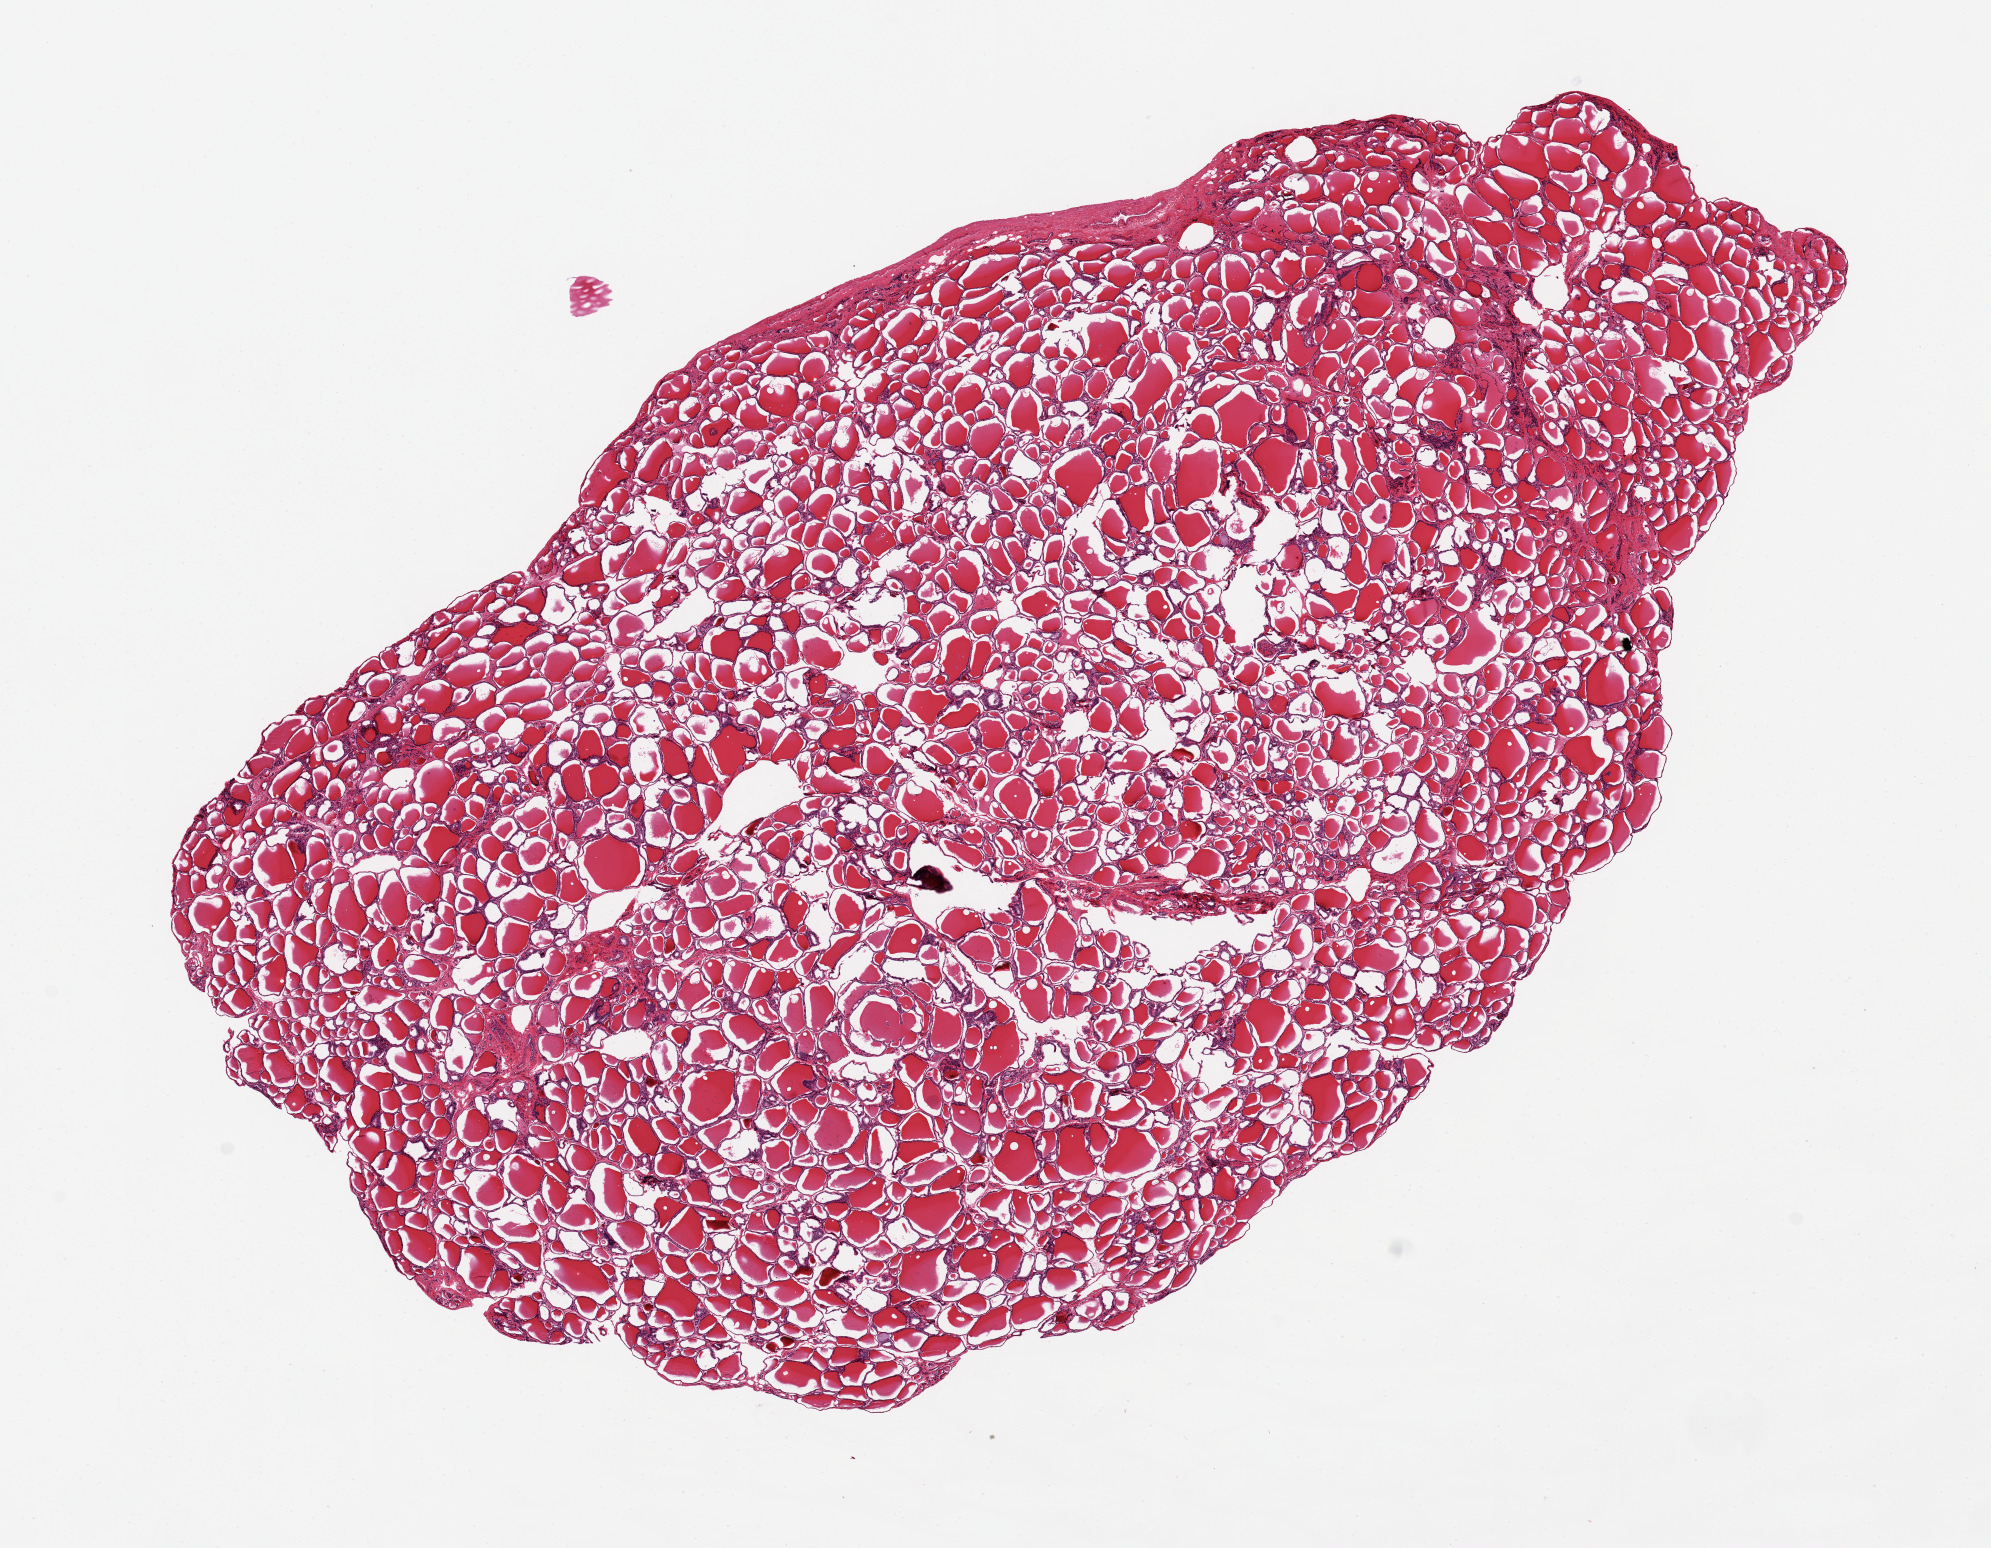
H&E whole-slide image, brightfield — whole scanned area (about 15.8 x 12.2 mm) shown as a low-resolution overview, PAXgene-fixed paraffin-embedded (PFPE) section, target tissue: thyroid, donor tissue sample. Donor sex: male.
Reviewer comment on this tissue sample: 1. 13.2x8mm. A few central holes.